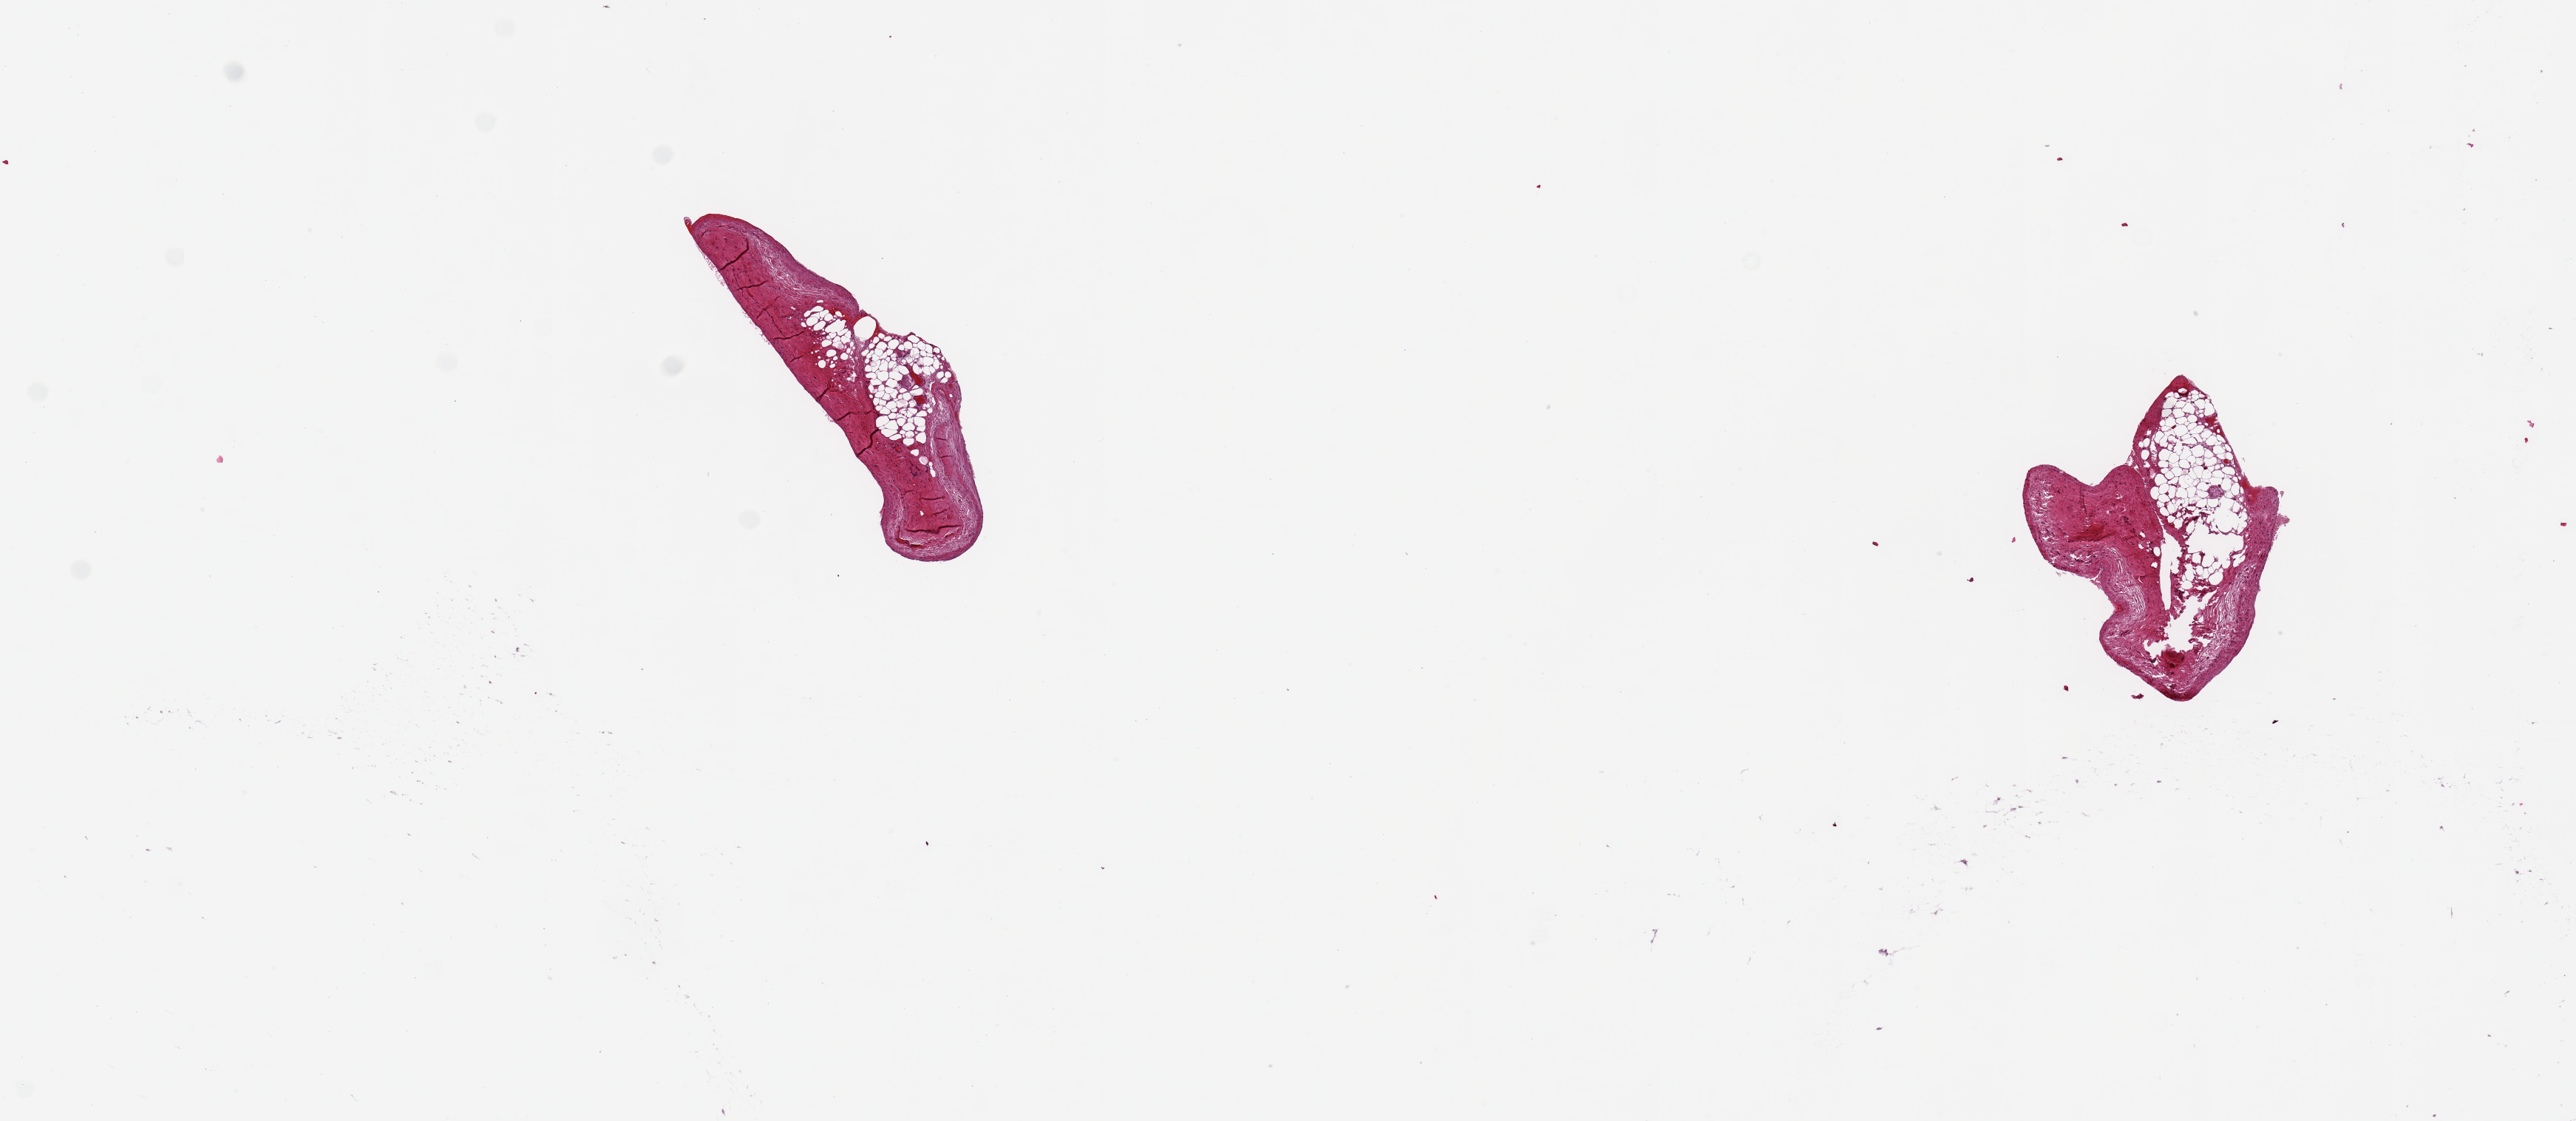
H&E whole-slide image — low-resolution overview of the scanned area, about 13.8 x 6.0 mm, PAXgene-fixed, paraffin-embedded tissue, target tissue: coronary artery, tissue donor sample. Male donor.
• reviewer comment on this tissue sample: 2 pieces fibroadipose tissue, no vessel present